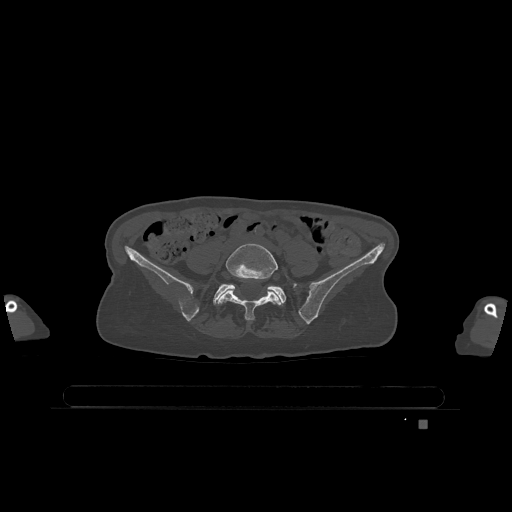
CT including the spine, one axial slice; position 226 of 1317 along the scan axis; bone window (W 1800 / L 400 HU); 0.5 mm slice thickness; 512 × 512 image matrix, field of view 500 × 500 mm. Female patient, age 74 years. Case-level facts recorded for this patient, not image findings: primary cancer: lung; vertebrae with lytic lesions (as recorded): T1, T4, T5, T6, L4, L5.
Structures marked on this image (semi-automatically segmented with operator editing):
- L5 vertebra: bounding box (x1, y1, x2, y2) in pixels: (217, 243, 288, 321)